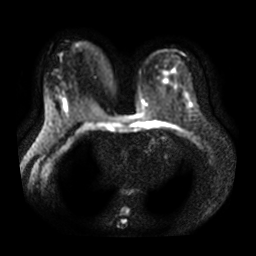
Breast MRI, one axial slice. Diffusion-weighted series; image 2 of 4 stored at this slice position (different b-values; order by instance number). 3 T. 5 mm slice thickness. 256 × 256 image matrix, field of view 360 × 360 mm. Female patient.
Outlined on this slice (expert manual segmentation):
- tumour on diffusion-weighted imaging: bounding box (x1, y1, x2, y2) in pixels: (63, 101, 68, 110)